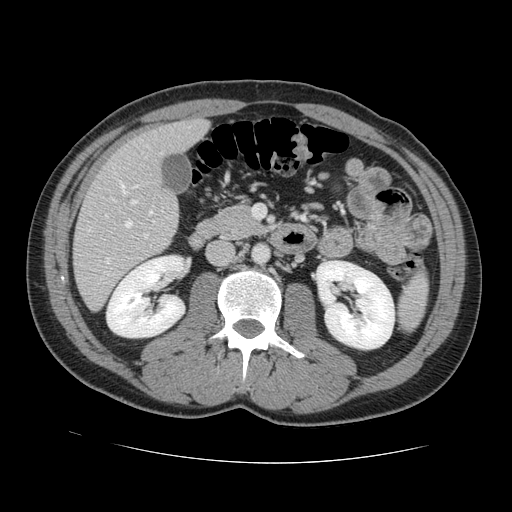
Contrast-enhanced abdominal CT, one axial slice; 120 kVp; soft-tissue window (W 400 / L 40 HU); 2.5 mm slice thickness; 512 × 512 image matrix, field of view 380 × 380 mm. Male patient, age 40 years. Case-level facts recorded for this patient, not image findings: diagnosis: colorectal cancer liver metastases, imaged before liver resection; multiple liver metastases: yes; largest metastasis: 2.9 cm; disease in both lobes: yes.
Annotated regions visible in this slice (expert manual segmentation):
- hepatic veins: box from (x=105, y=153) to (x=162, y=264) px
- liver: (x=74, y=120)–(x=207, y=309)
- planned liver remnant (the part of the liver to remain after resection): (x=117, y=120)–(x=208, y=171)
- portal vein (with intrahepatic branches): (x=131, y=200)–(x=148, y=238)